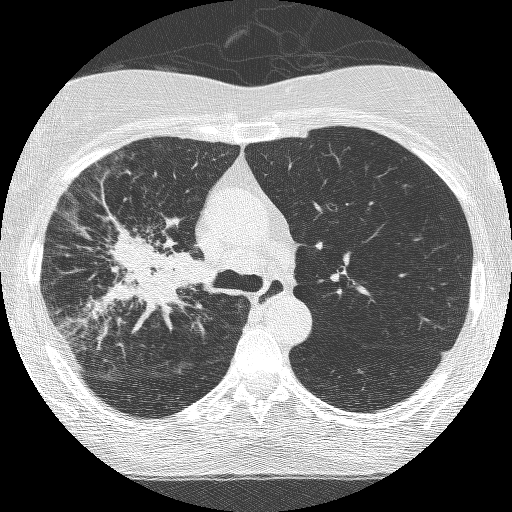
Chest CT (low-dose screening protocol), one axial image; third screening round (two years after baseline); lung window (W 1500 / L -600 HU); 1.25 mm slice thickness; slice 174 of 253 in the series. Female participant, aged 64 years at enrolment. Former smoker at enrolment.
Expert-annotated lung lesion, bounding box [x1, y1, x2, y2] px = [89, 220, 205, 336]. Screening reader's record for this exam (one nodule recorded; not confirmed to be the boxed lesion): non-calcified nodule or mass ≥4 mm, right upper lobe, 49 × 43 mm, spiculated (stellate) margins, soft tissue attenuation, pre-existing on the prior screen: yes; interval growth: yes. Official screen result: positive, other.